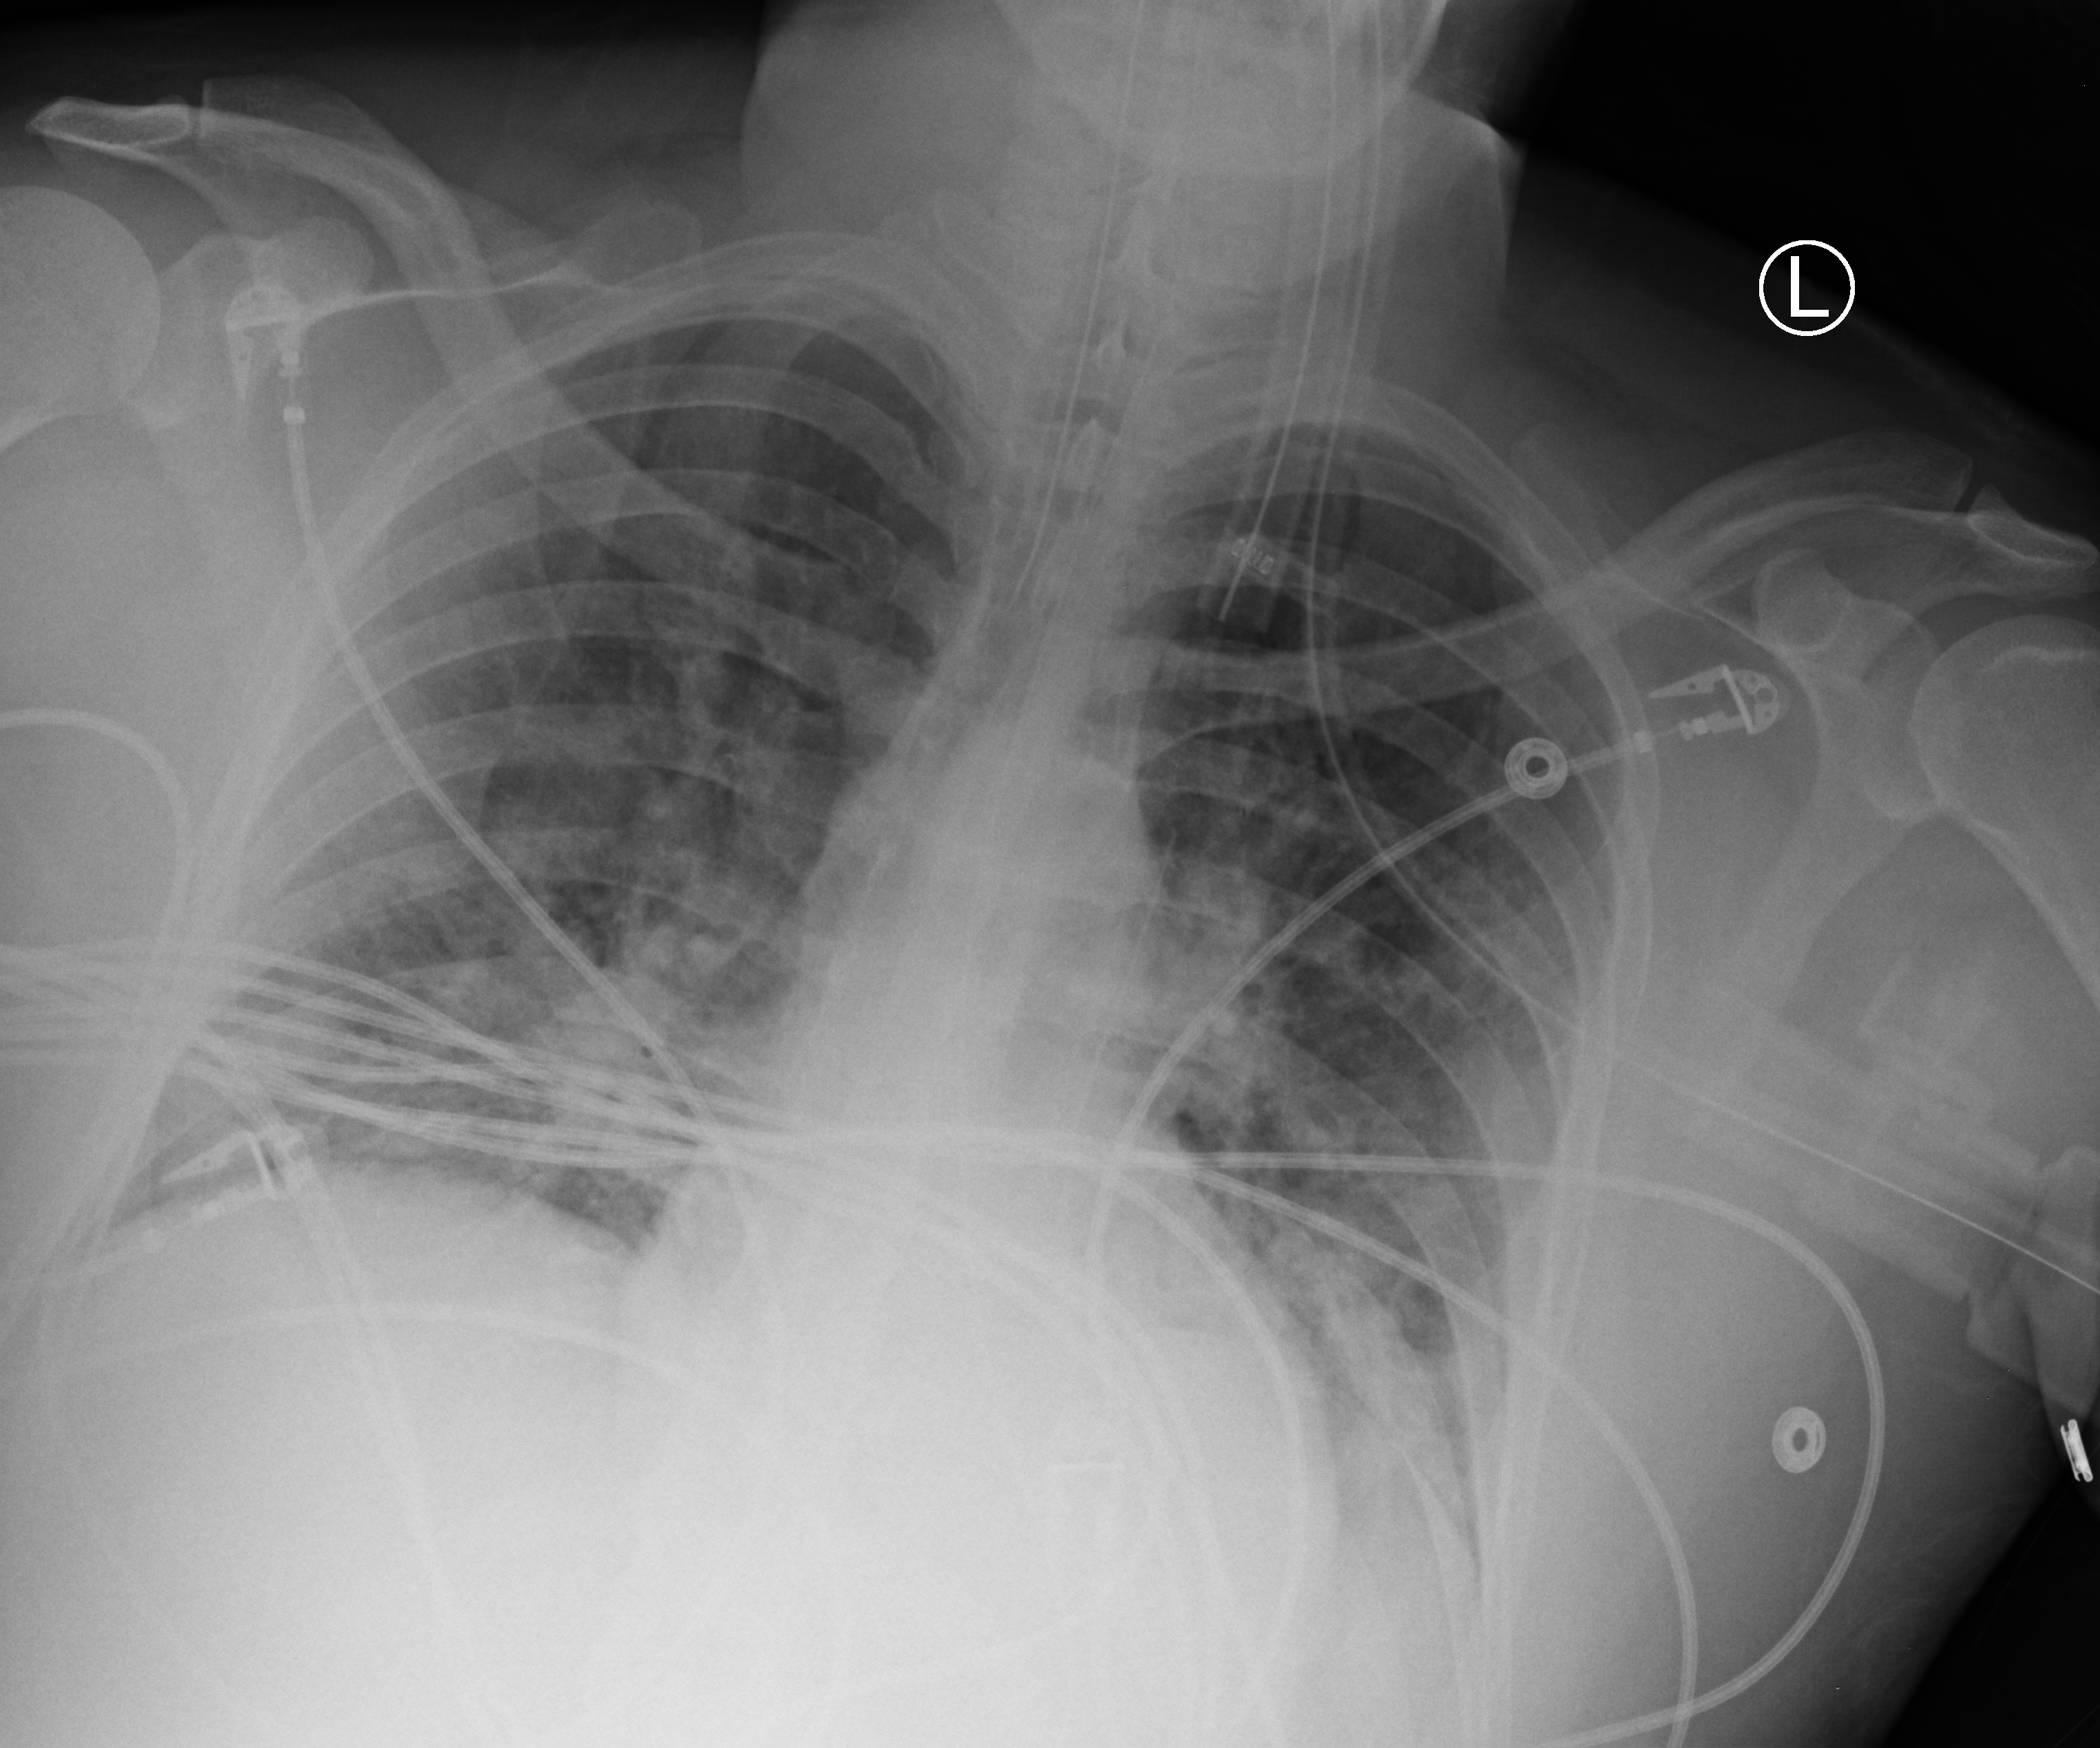
Portable chest radiograph; anteroposterior (AP) projection. Male patient hospitalised with COVID-19, age 18–59 years.
From the hospital-stay record, not from the radiograph (when in the stay this image was taken is not recorded): smoking status (admission record): never.